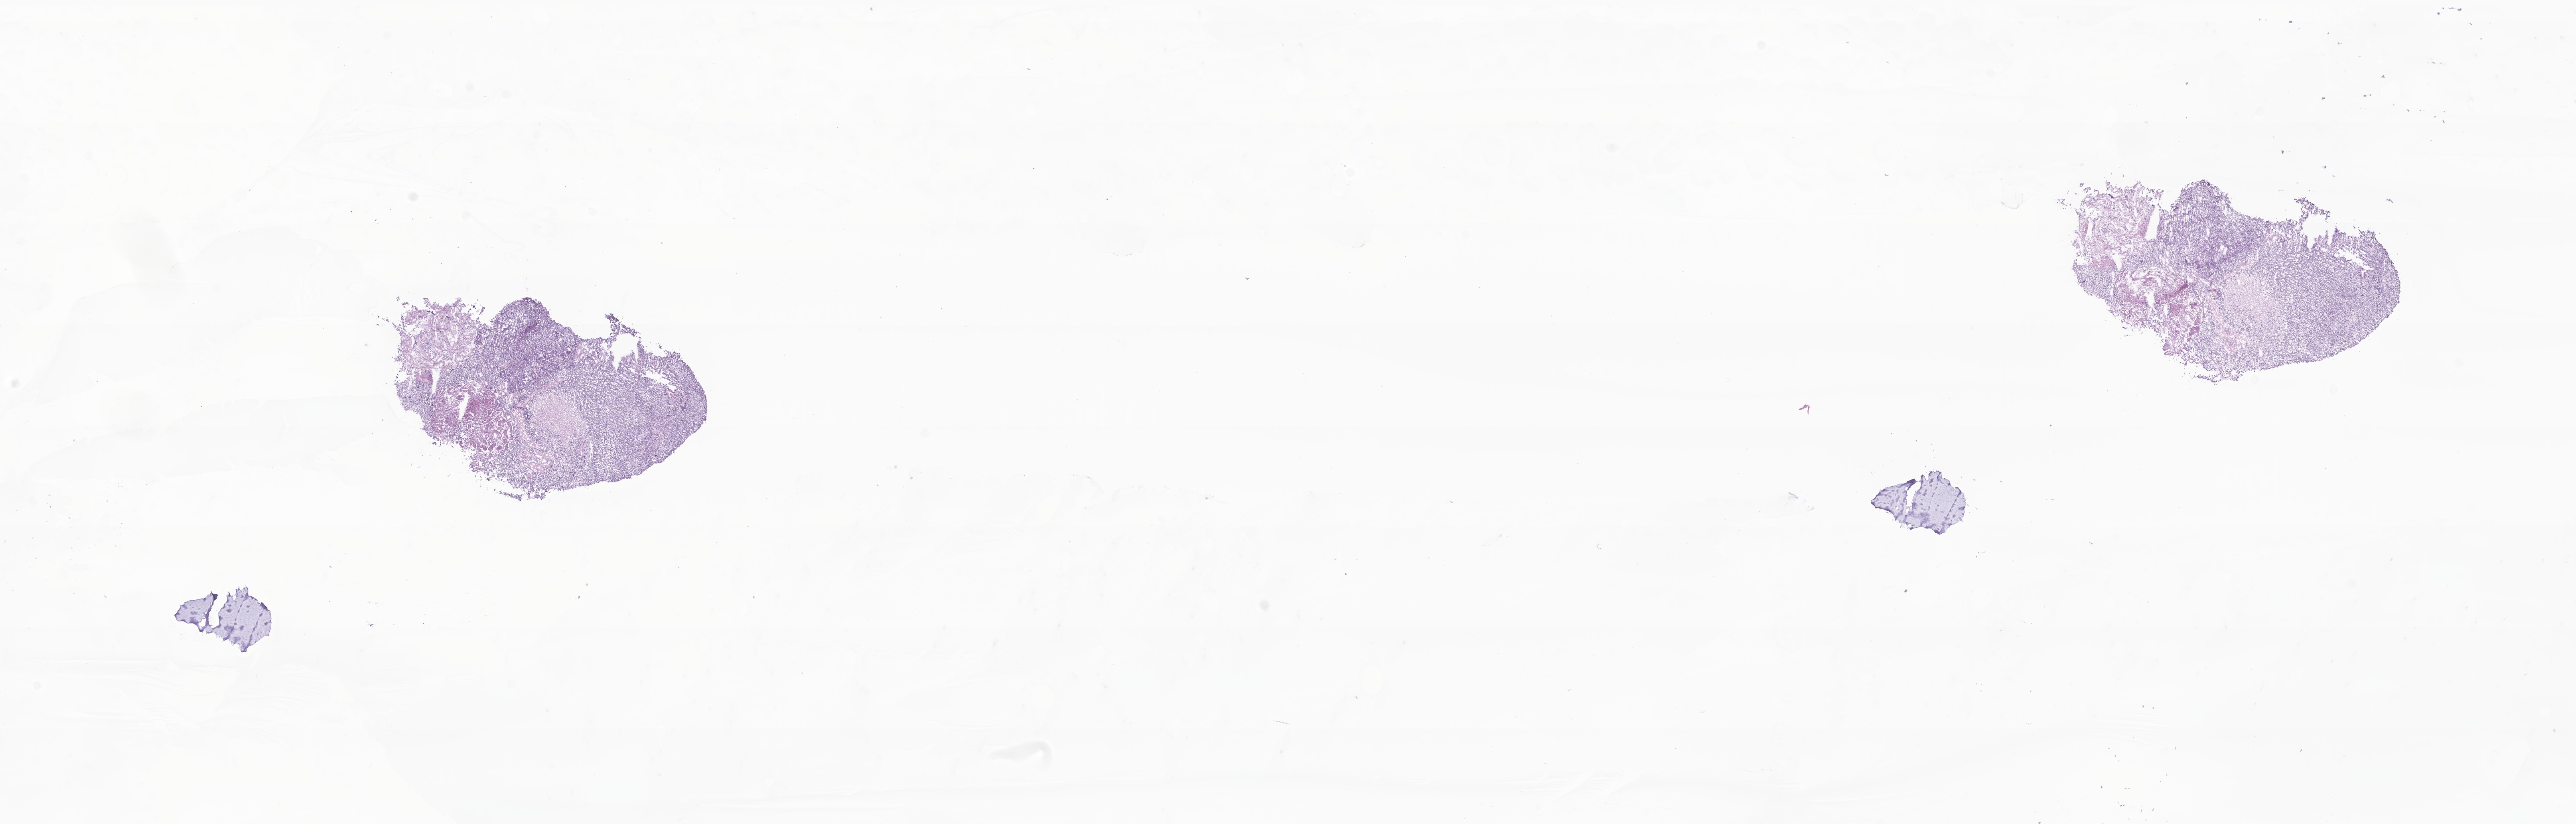
H&E whole-slide image of tumor tissue from the brain, low-resolution overview of the scanned area, about 27.2 x 8.7 mm; frozen section (OCT-embedded). Patient male; age 982 days.
• diagnosis: Medulloblastoma, NOS